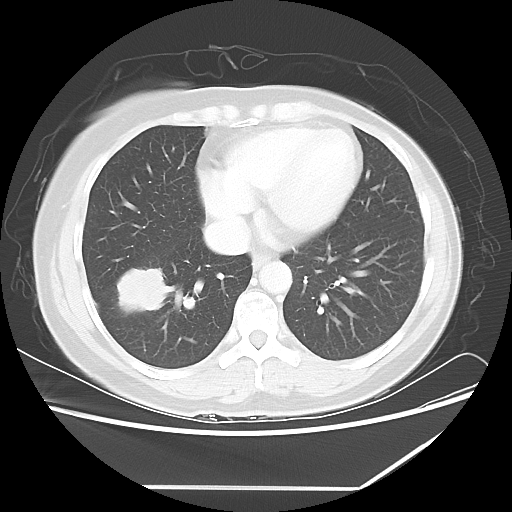
Chest CT, one axial slice. Position 23 of 60 along the scan axis. 100 kVp. Lung window (W 1500 / L -600 HU). 5 mm slice thickness. 512 × 512 image matrix, field of view 374 × 374 mm. Patient: female, 42 years. From the clinical record (not read from this slice): clinical TNM (as recorded): T2 N1 M0.
Outlined on this slice (rectangle marked by the reading radiologist):
- lung tumour (recorded histology: adenocarcinoma): bounding box (x1, y1, x2, y2) in pixels: (107, 260, 173, 323)